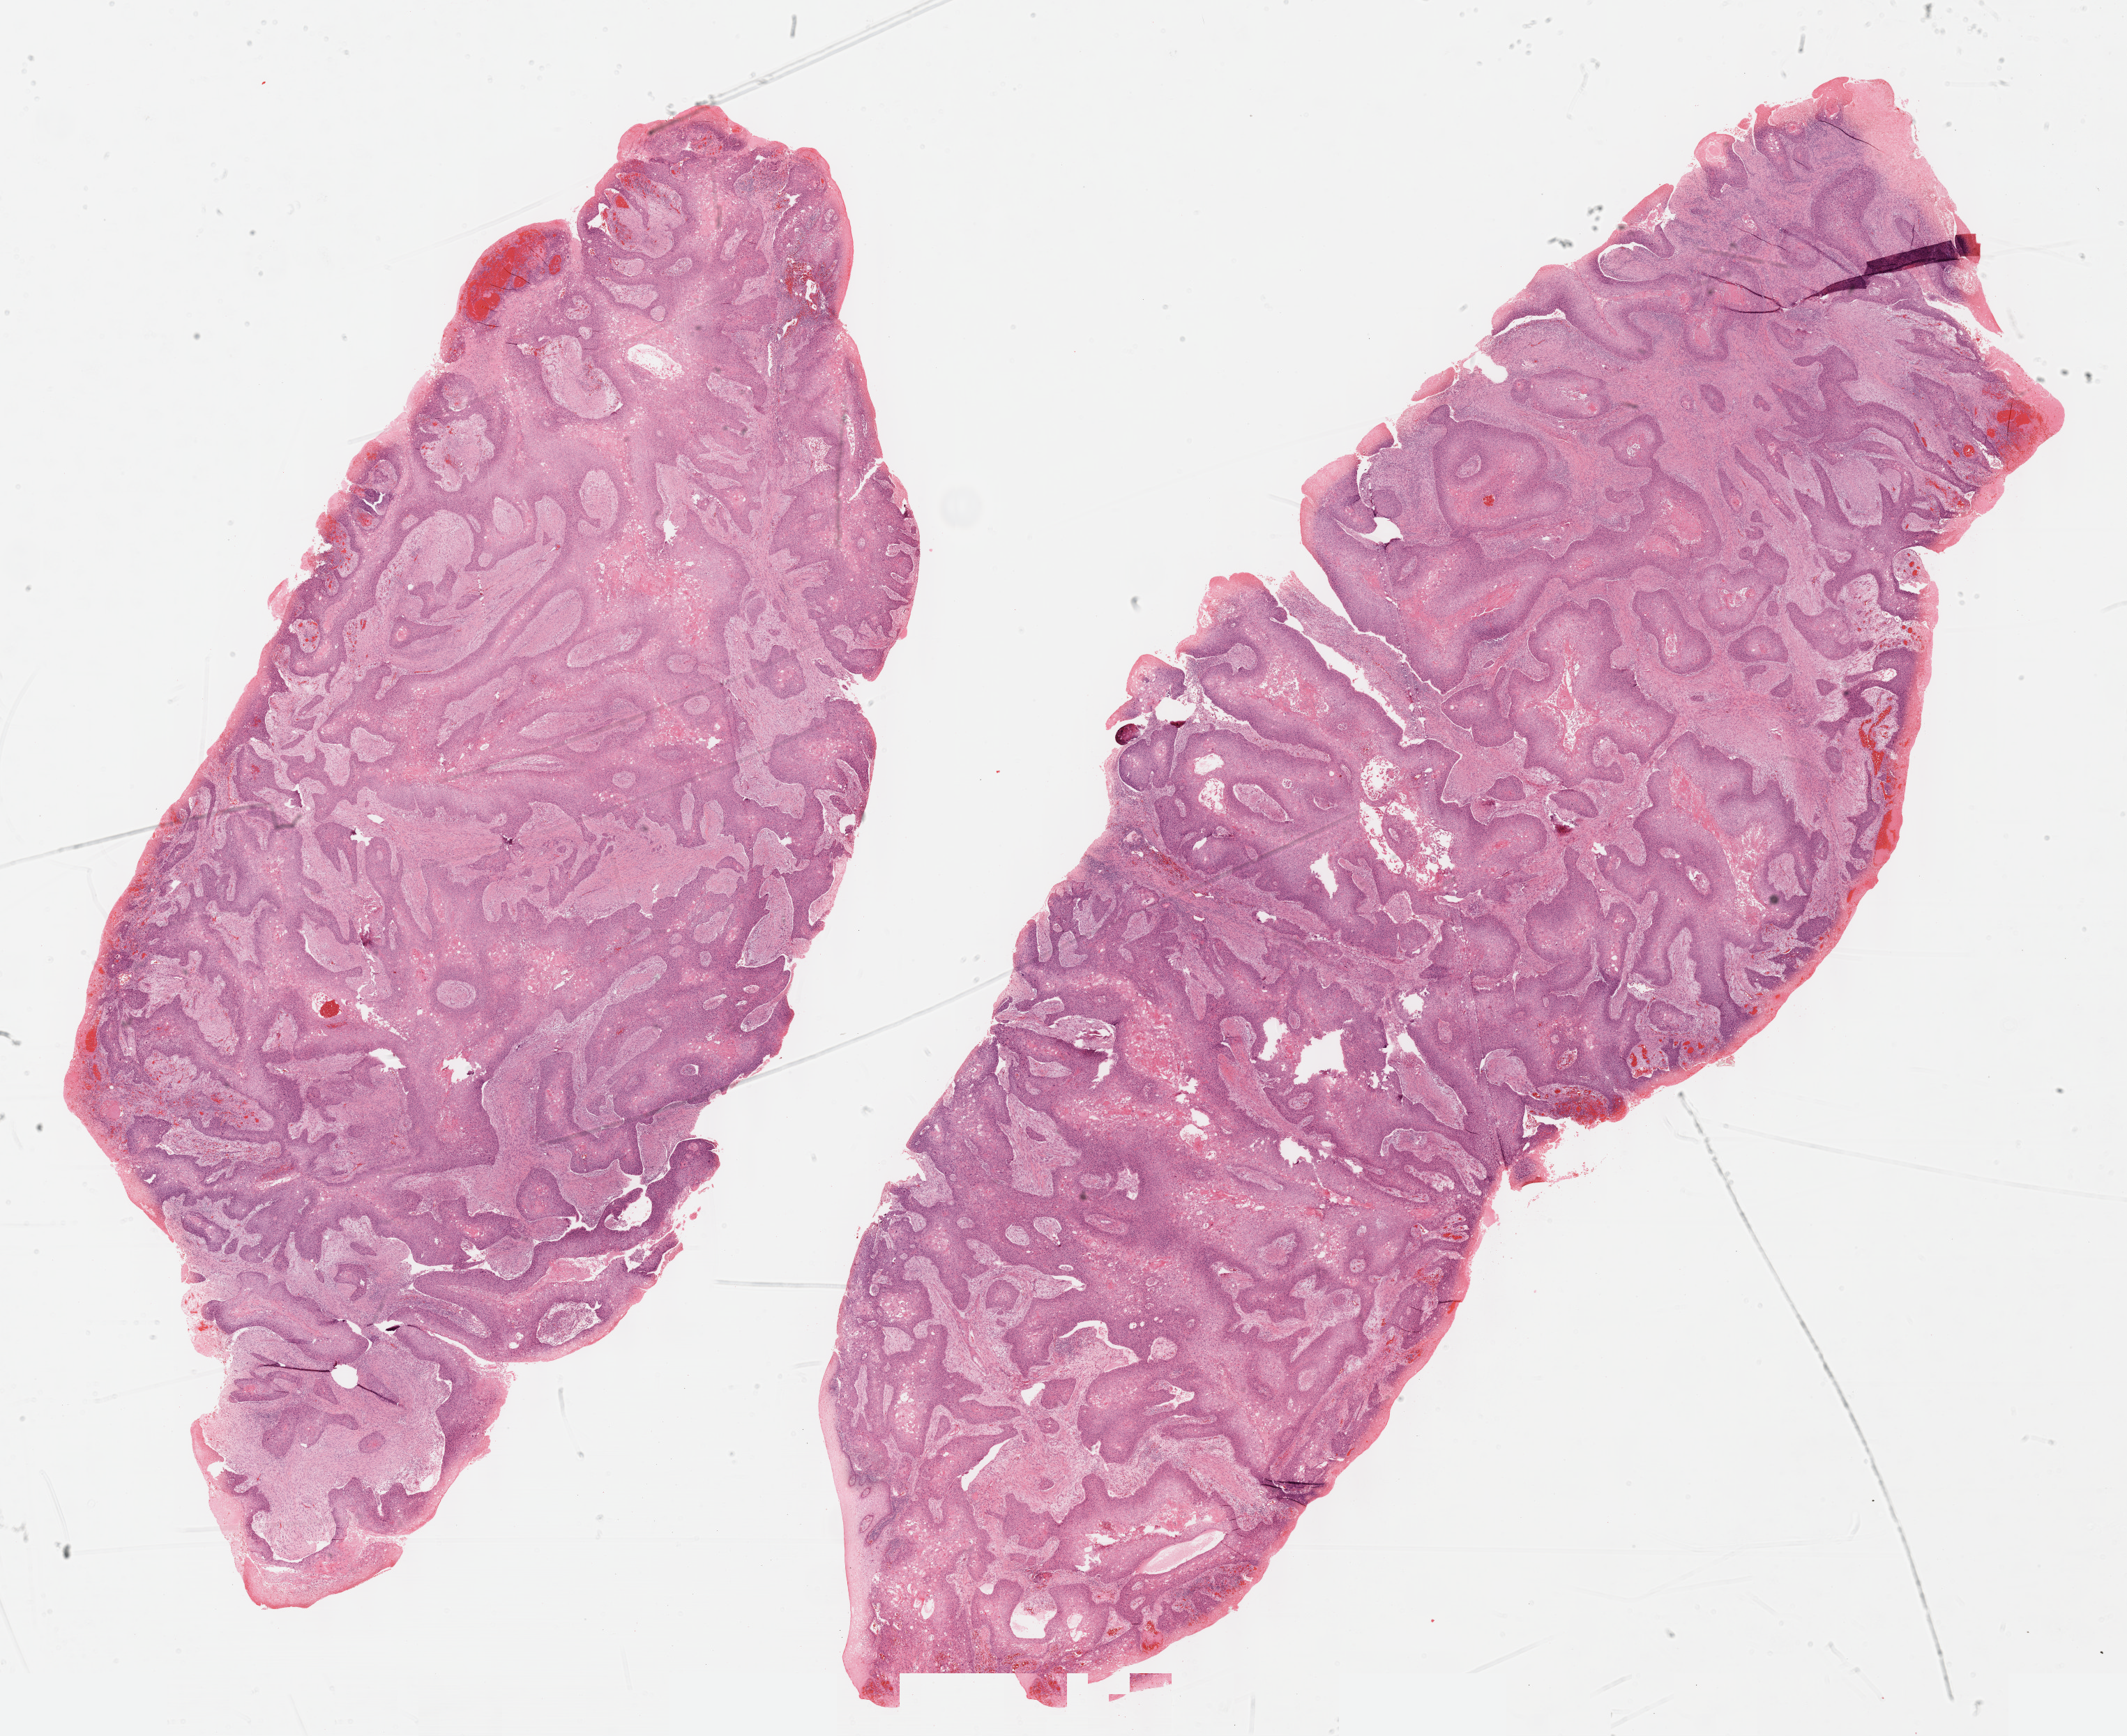
H&E-stained whole-slide image, shown as a low-resolution overview of the whole scanned area (about 24.6 x 20.1 mm), formalin-fixed paraffin-embedded (FFPE) diagnostic section, sample: primary tumour, head and neck. Male, age 54 years at initial diagnosis.
Pathologic diagnosis: Squamous cell carcinoma, NOS.